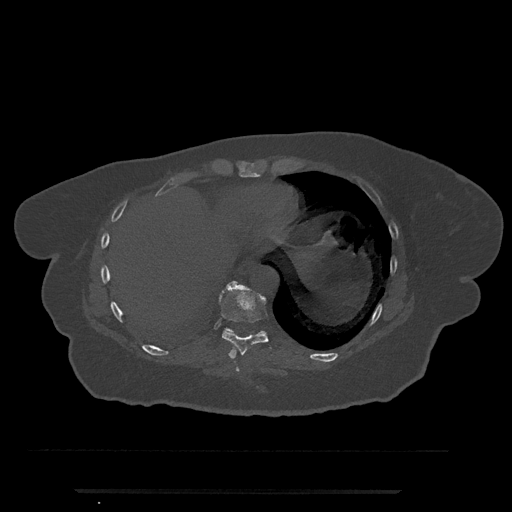
CT including the spine, one axial slice. Slice 329 of 797 in the series (ordered by position). Bone window (W 1800 / L 400 HU). 512 × 512 image matrix. Patient: female, 51 years. From the clinical record (not read from this slice): primary cancer: neuro.
Structures marked on this image (semi-automatically segmented with operator editing):
- T10 vertebra: bounding box <225,328,264,335> (left, top, right, bottom; pixels)
- T8 vertebra: <235,367,240,372>
- T9 vertebra: <209,281,272,358>